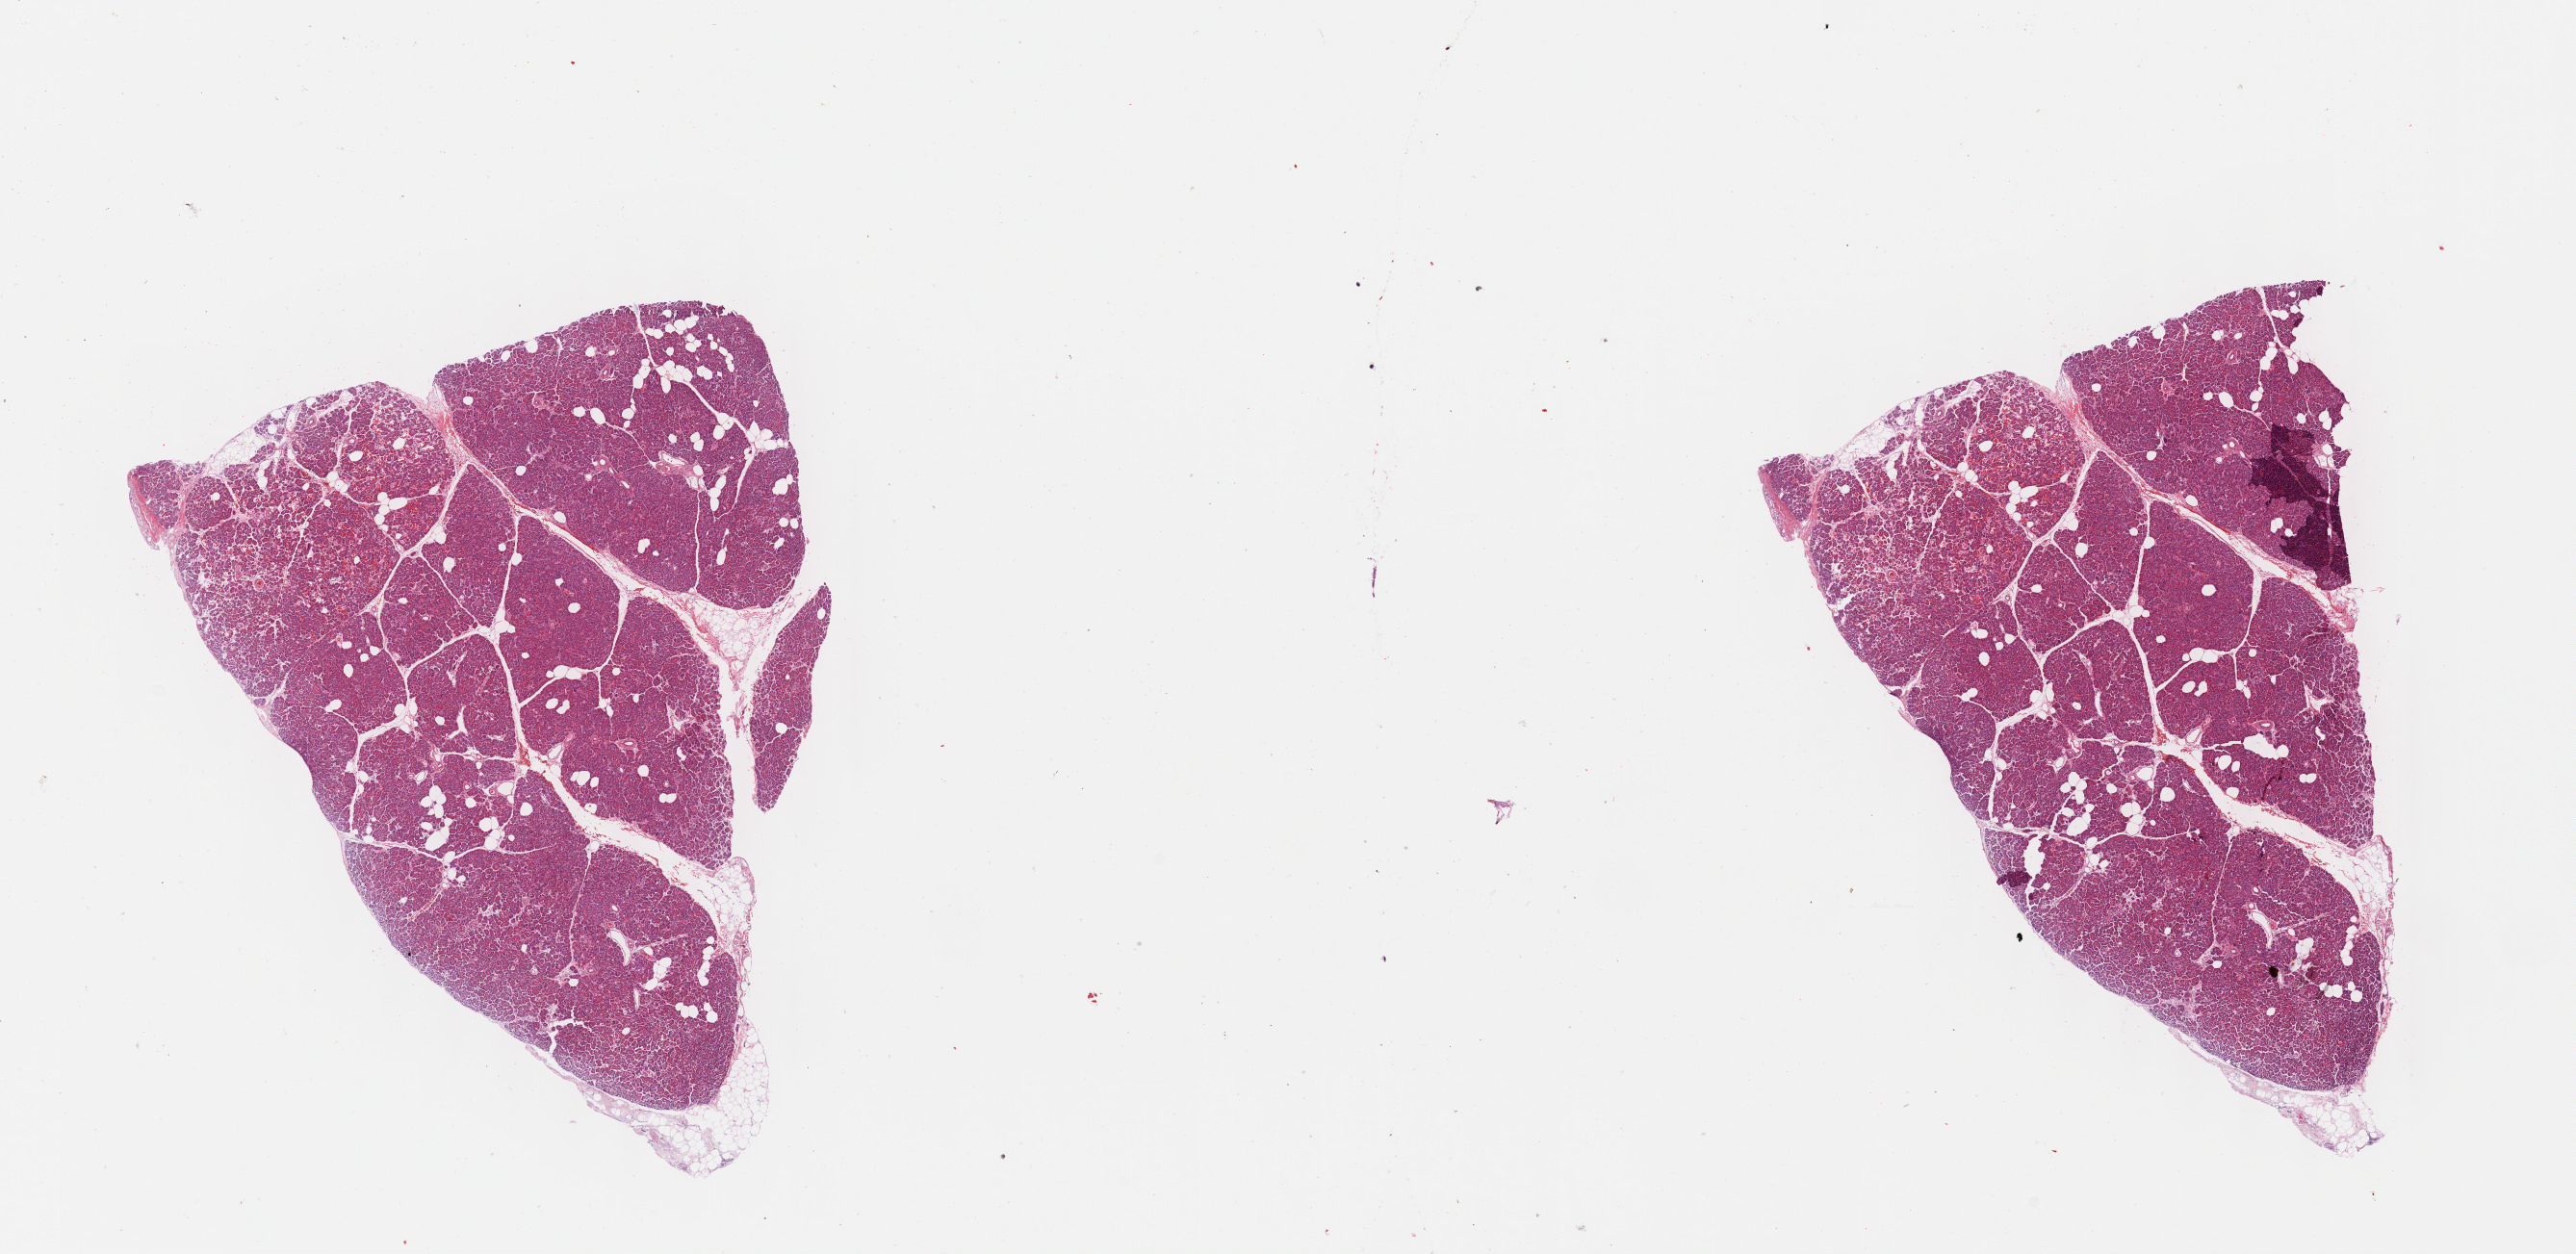
Digitized H&E tissue section (whole slide), whole scanned area (about 21.6 x 10.5 mm, slide scanned at 40x) shown as a low-resolution overview. Formalin-fixed paraffin-embedded (FFPE) diagnostic section. Solid tissue normal (non-tumour tissue) sample from the pancreas. Patient: female, age at initial diagnosis 72 years.
This section: solid tissue normal (non-tumour) sample from the same patient. Patient diagnosis: Infiltrating duct carcinoma, NOS (tail of pancreas).